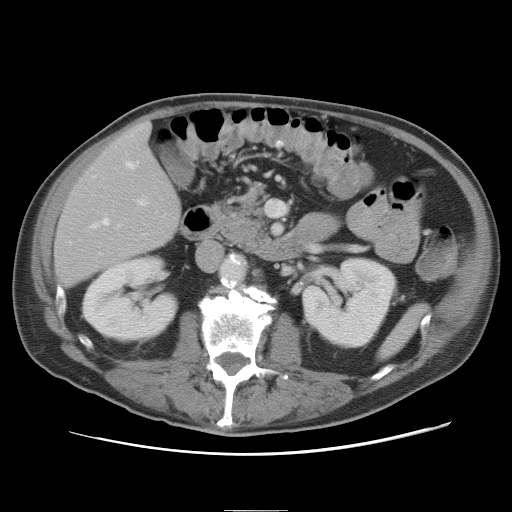
Contrast-enhanced abdominal CT, one axial slice. Position 26 of 89 along the scan axis. Intravenous contrast given. Soft-tissue window (W 400 / L 40 HU). 5 mm slice thickness. 512 × 512 image matrix, field of view 375 × 375 mm. Male patient, age 69 years. Case-level facts recorded for this patient, not image findings: diagnosis: colorectal cancer liver metastases, imaged before liver resection; multiple liver metastases: no; largest metastasis: 8.5 cm; disease in both lobes: no.
Structures marked on this image (outlined manually by an expert reader):
- hepatic veins: box from (x=93, y=162) to (x=139, y=228) px
- liver: (x=55, y=123)–(x=181, y=289)
- planned liver remnant (the part of the liver to remain after resection): (x=55, y=123)–(x=181, y=288)
- portal vein (with intrahepatic branches): (x=137, y=199)–(x=148, y=206)